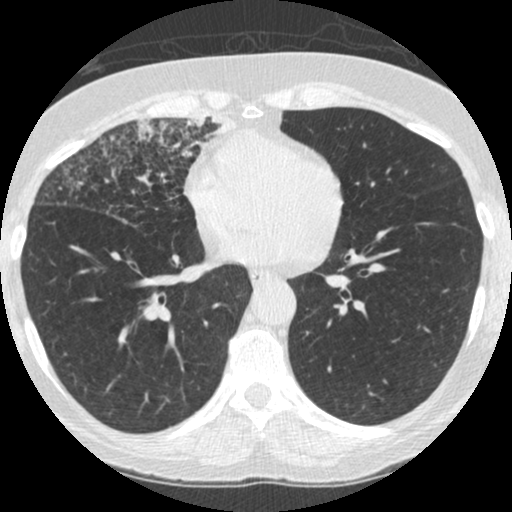
Low-dose screening chest CT, one axial slice; reconstruction kernel STANDARD; 120 kVp; lung window (W 1500 / L -600 HU); 1.25 mm slice thickness; 512 × 512 image matrix.
Annotated regions visible in this slice (outlined manually by an expert reader):
- lesion 4 (tumor, upper lobe of right lung): bounding box (x1, y1, x2, y2) in pixels: (186, 114, 232, 145)